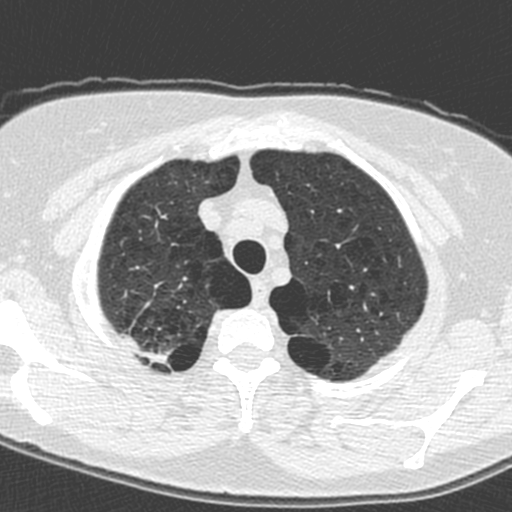
Low-dose screening chest CT, axial slice, baseline screening round, lung window (W 1500 / L -600 HU), standard (soft-tissue) reconstruction kernel (C), slice 19 of 224 in the series. Female, age 59 years at enrolment. Current smoker at enrolment.
- Lesion marked by an expert reader, bounding box <132,331,178,377> (left, top, right, bottom; pixels).
- No non-calcified nodule or mass ≥4 mm was recorded by the screening reader at this exam.
- Participant outcome: lung cancer diagnosed 881 days after this screen (after the third annual screen) — adenocarcinoma, NOS, right upper lobe, poorly differentiated (G3), stage IA (AJCC 6th edition), 20 mm at pathology.